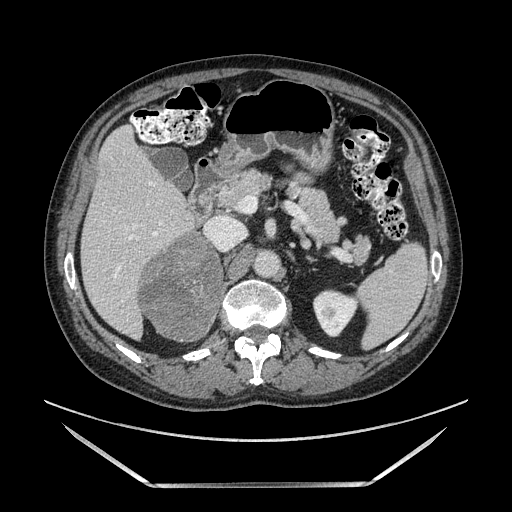
Contrast-enhanced abdominal CT, one axial slice. Soft-tissue window (W 400 / L 40 HU). 1.25 mm slice thickness. 512 × 512 image matrix, field of view 440 × 440 mm. Male patient. Case-level facts recorded for this patient, not image findings: diagnosis: adrenocortical carcinoma; tumour side: right adrenal; tumour size at pathology: 10.3 cm; Ki-67 index: 20 %; stage (as recorded): 3.
Outlined on this slice (semi-automatic segmentation, software-assisted and operator-edited):
- mass: bounding box <139,235,217,337> (left, top, right, bottom; pixels)